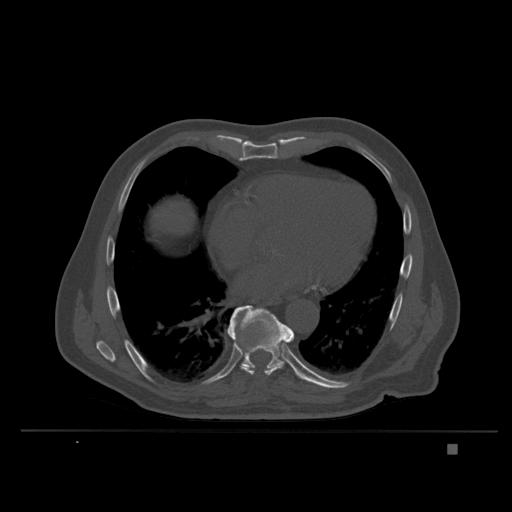
CT including the spine, one axial slice. Position 221 of 435 along the scan axis. Bone window (W 1800 / L 400 HU). 1.5 mm slice thickness. 512 × 512 image matrix, field of view 434 × 434 mm. Patient: male, 73 years. Case-level facts recorded for this patient, not image findings: primary cancer: skin.
Outlined on this slice (semi-automatically segmented with operator editing):
- T6 vertebra: box from (x=234, y=329) to (x=289, y=352) px
- T8 vertebra: (x=228, y=321)–(x=294, y=376)
- T9 vertebra: (x=228, y=305)–(x=305, y=380)